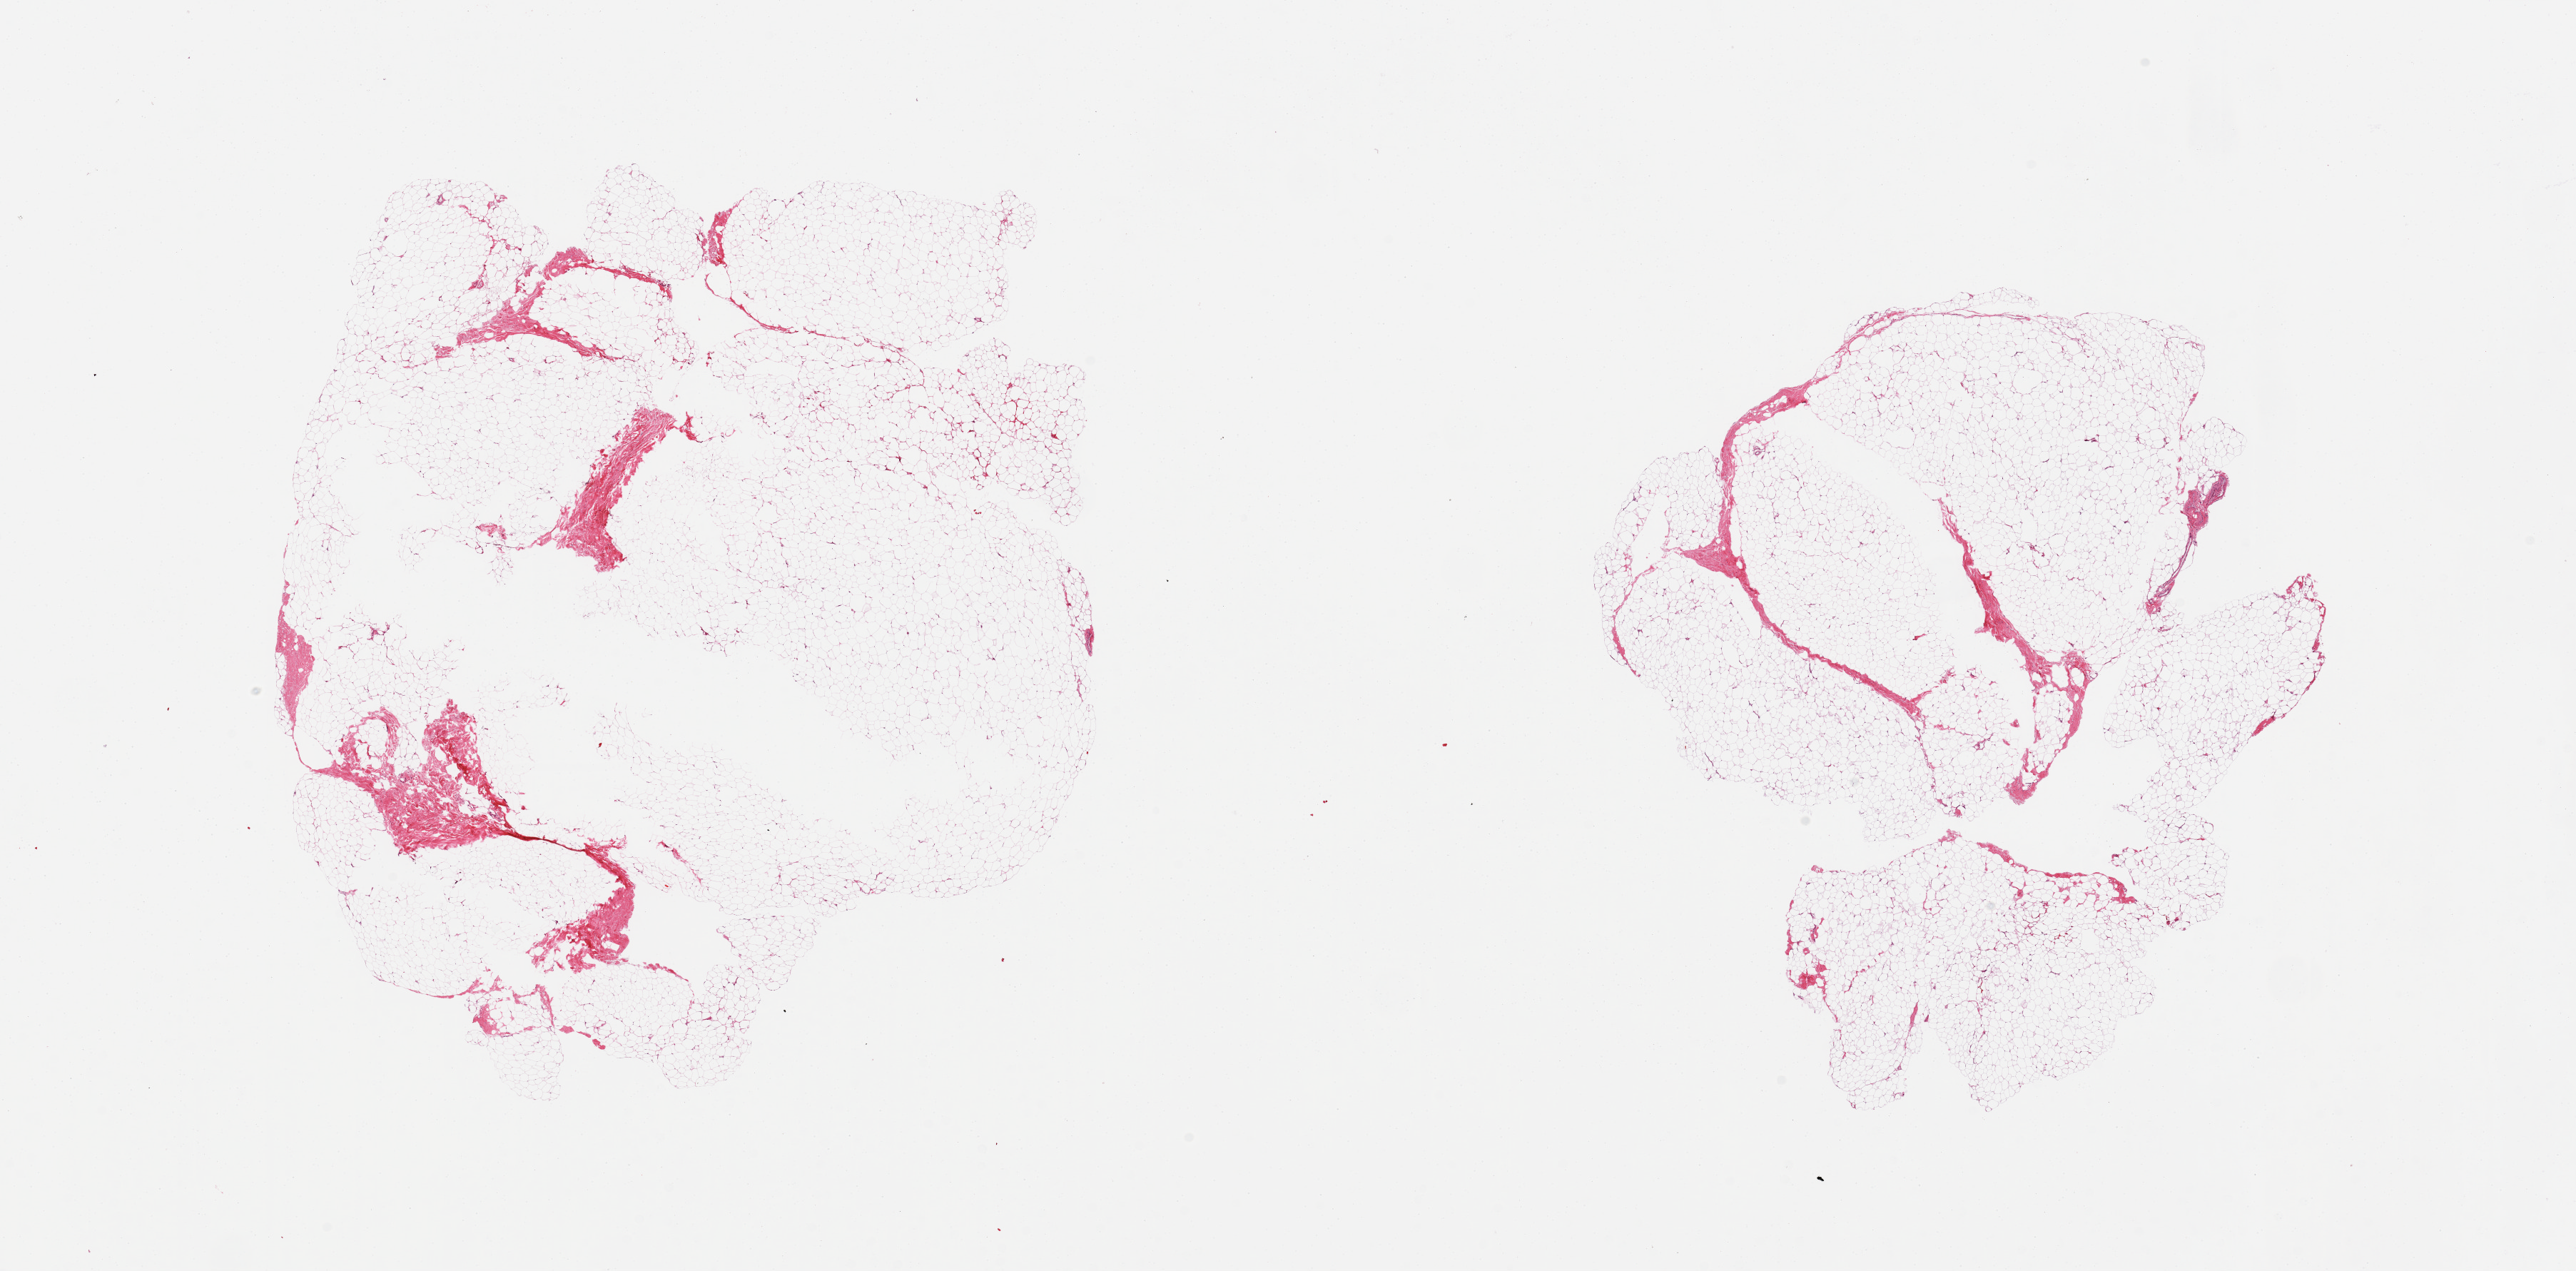
Digitized hematoxylin and eosin (H&E)-stained section — low-resolution overview of the scanned area, about 28.5 x 14.1 mm (from a 20x scan). PAXgene-fixed paraffin-embedded (PFPE) section. Sampled site (target tissue): breast. Donor tissue sample. Donor sex: male.
- review note (as recorded): 2 pieces, adipose tissue with <10% fibrous tissue, no epithelium, central defects in tissue